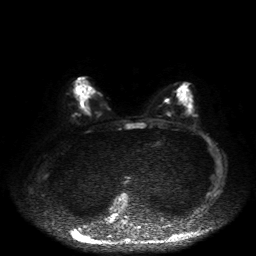
Breast MRI, one axial slice; slice 24 of 50 in the series (ordered by position); diffusion-weighted series; image 2 of 4 stored at this slice position (different b-values; order by instance number); 1.5 T; 4 mm slice thickness; 256 × 256 image matrix, field of view 360 × 360 mm. Female patient.
Annotated regions visible in this slice (outlined manually by an expert reader):
- tumour on diffusion-weighted imaging: bounding box <81,106,87,112> (left, top, right, bottom; pixels)